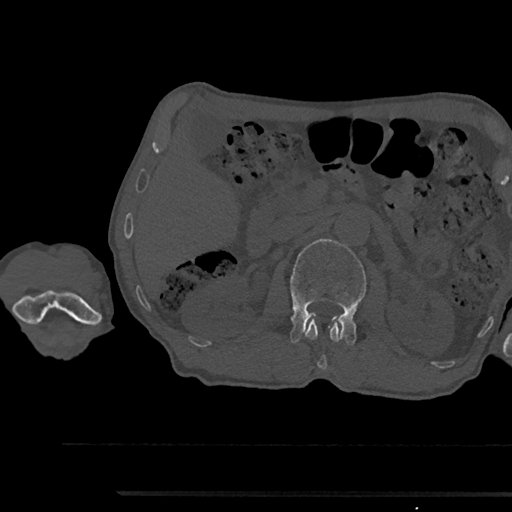
CT including the spine, one axial slice. Slice 593 of 797 in the series (ordered by position). Reconstruction kernel Br40s/3. Bone window (W 1800 / L 400 HU). 512 × 512 image matrix, field of view 367 × 367 mm. Male patient, age 79 years. Case-level facts recorded for this patient, not image findings: primary cancer: prostate.
Structures marked on this image (semi-automatic segmentation, software-assisted and operator-edited):
- L1 vertebra: bounding box <305,319,342,369> (left, top, right, bottom; pixels)
- L2 vertebra: <290,239,366,345>